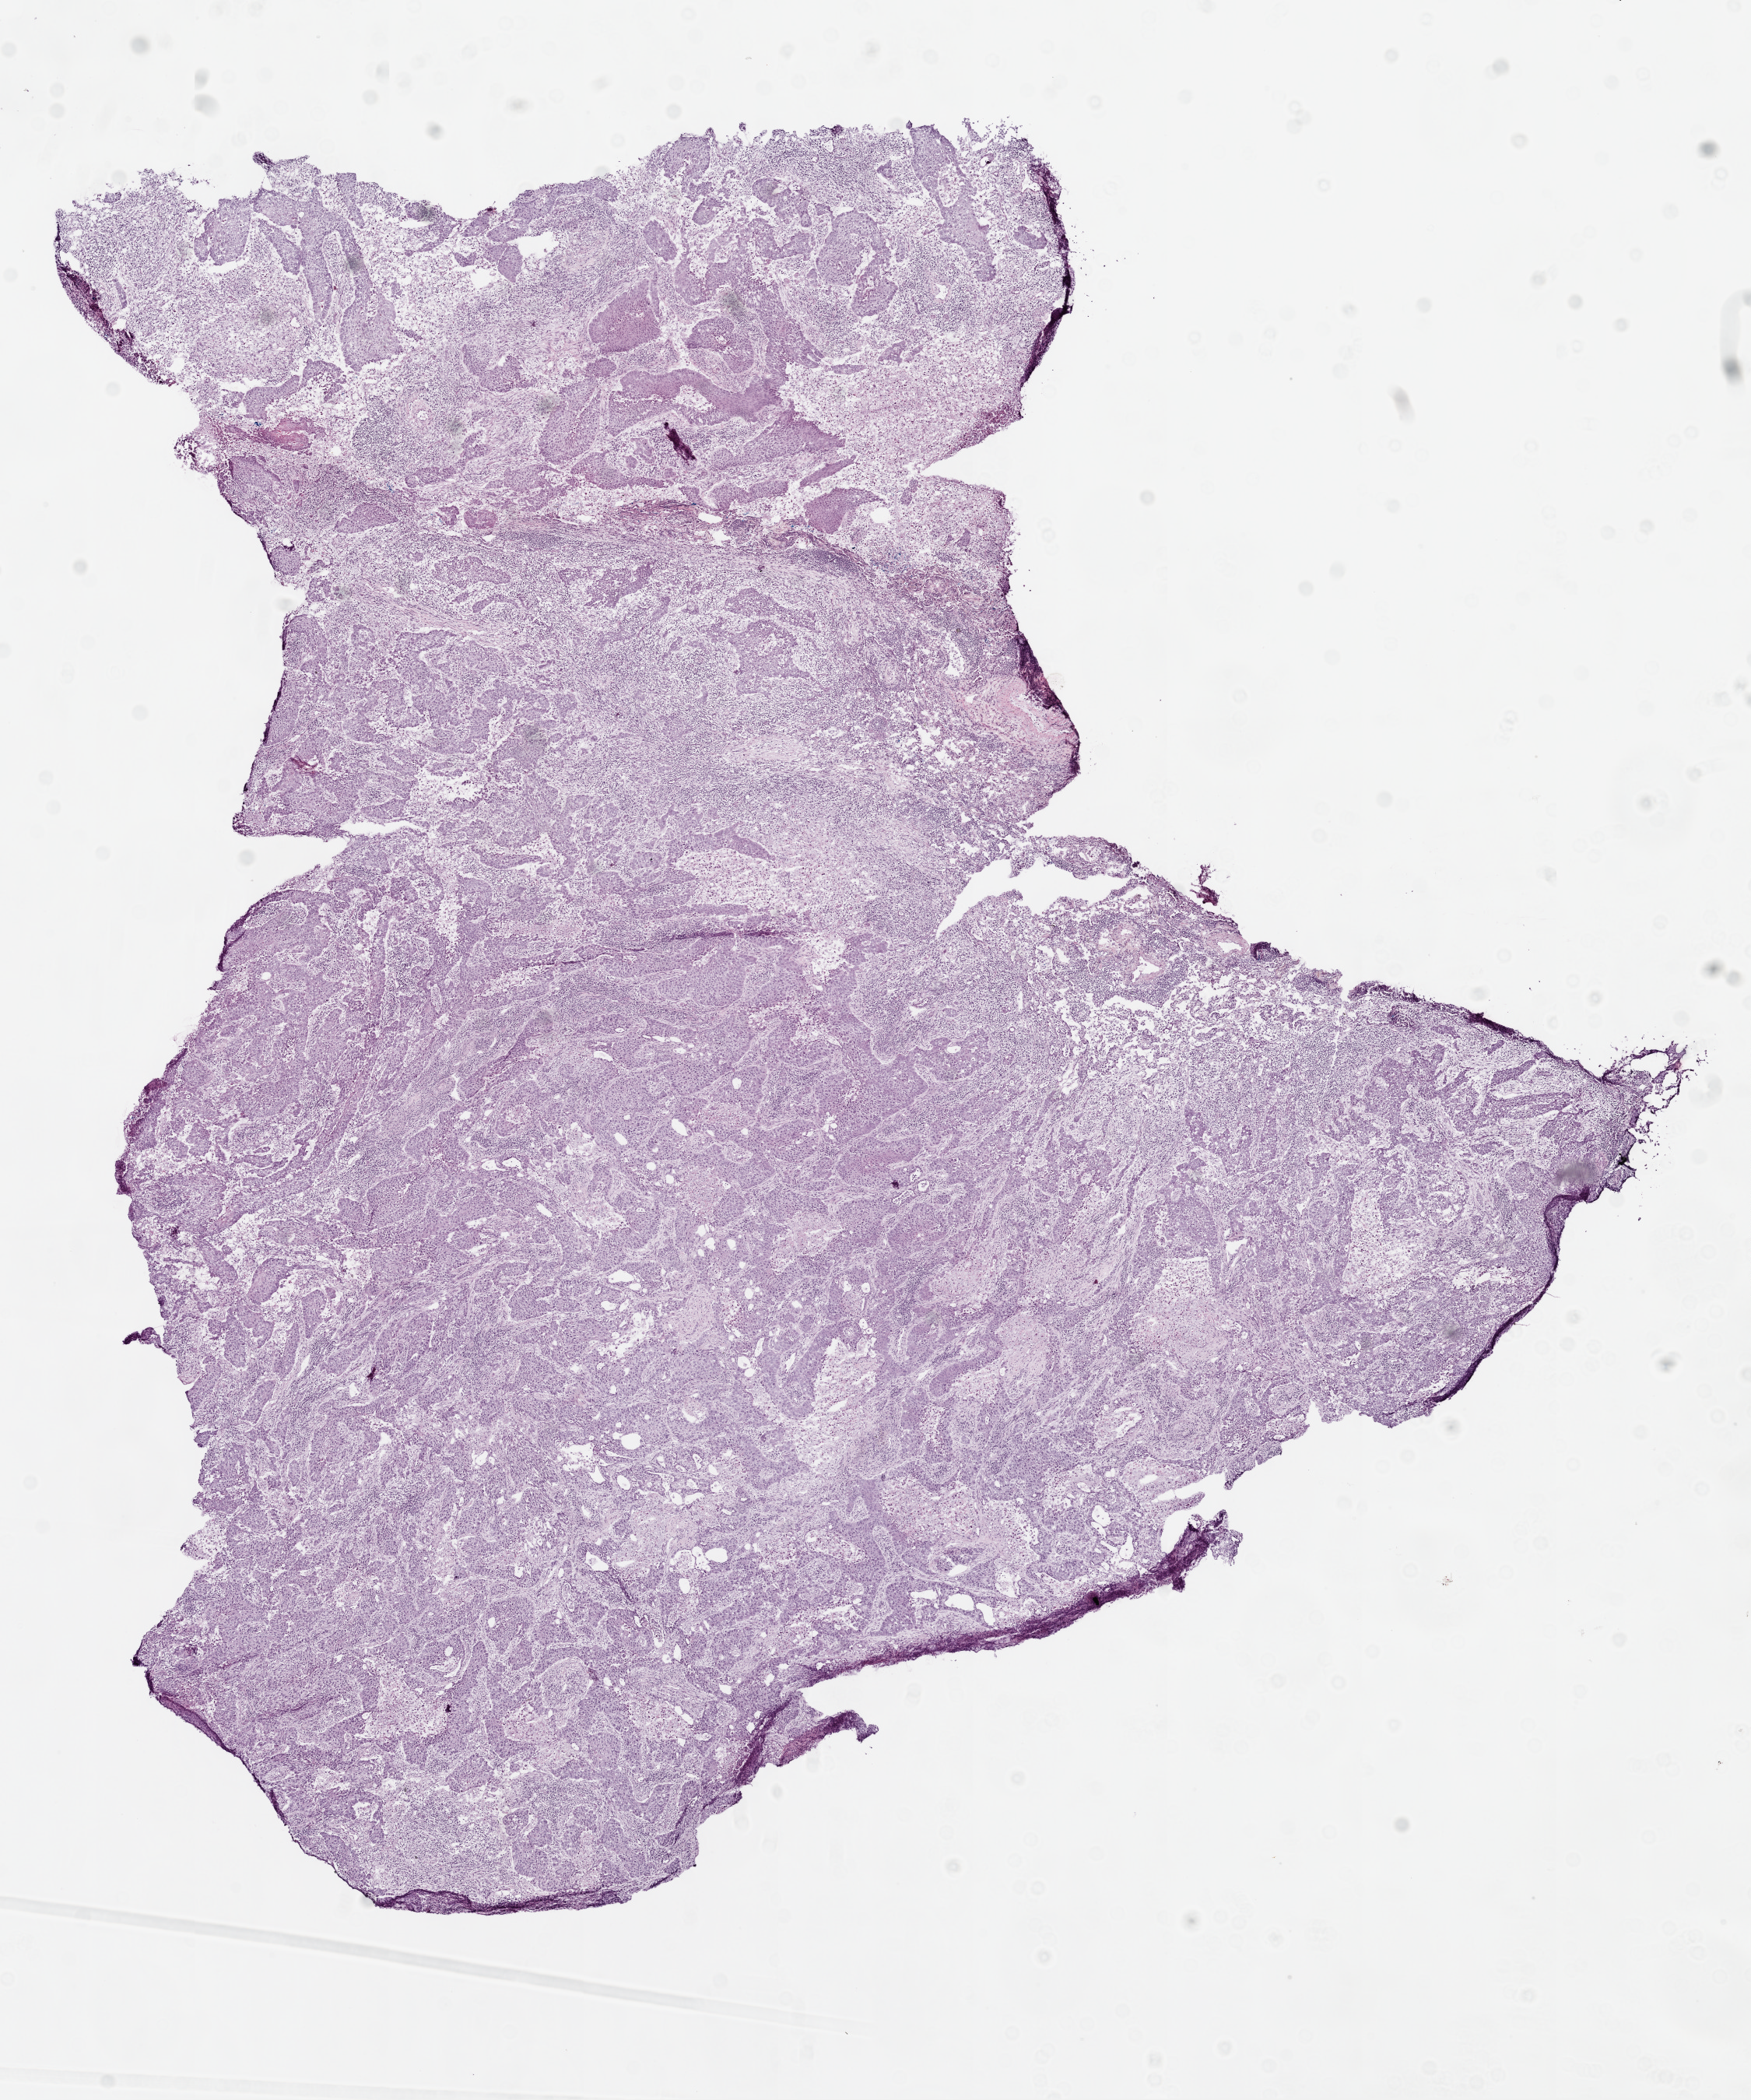
H&E-stained whole-slide image — whole scanned area (about 9.0 x 10.8 mm, from a 20x scan) shown as a low-resolution overview; frozen section from the top of the tissue portion; primary tumour sample from the lung. Patient: female, age at initial diagnosis 74 years. Slide review estimates, as recorded: tumour cells 75%, tumour nuclei 85%, normal cells 0%, stromal cells 10%, necrosis 15%.
* laterality: right
* pathologic diagnosis: Squamous cell carcinoma, NOS
* AJCC pathologic stage: IB